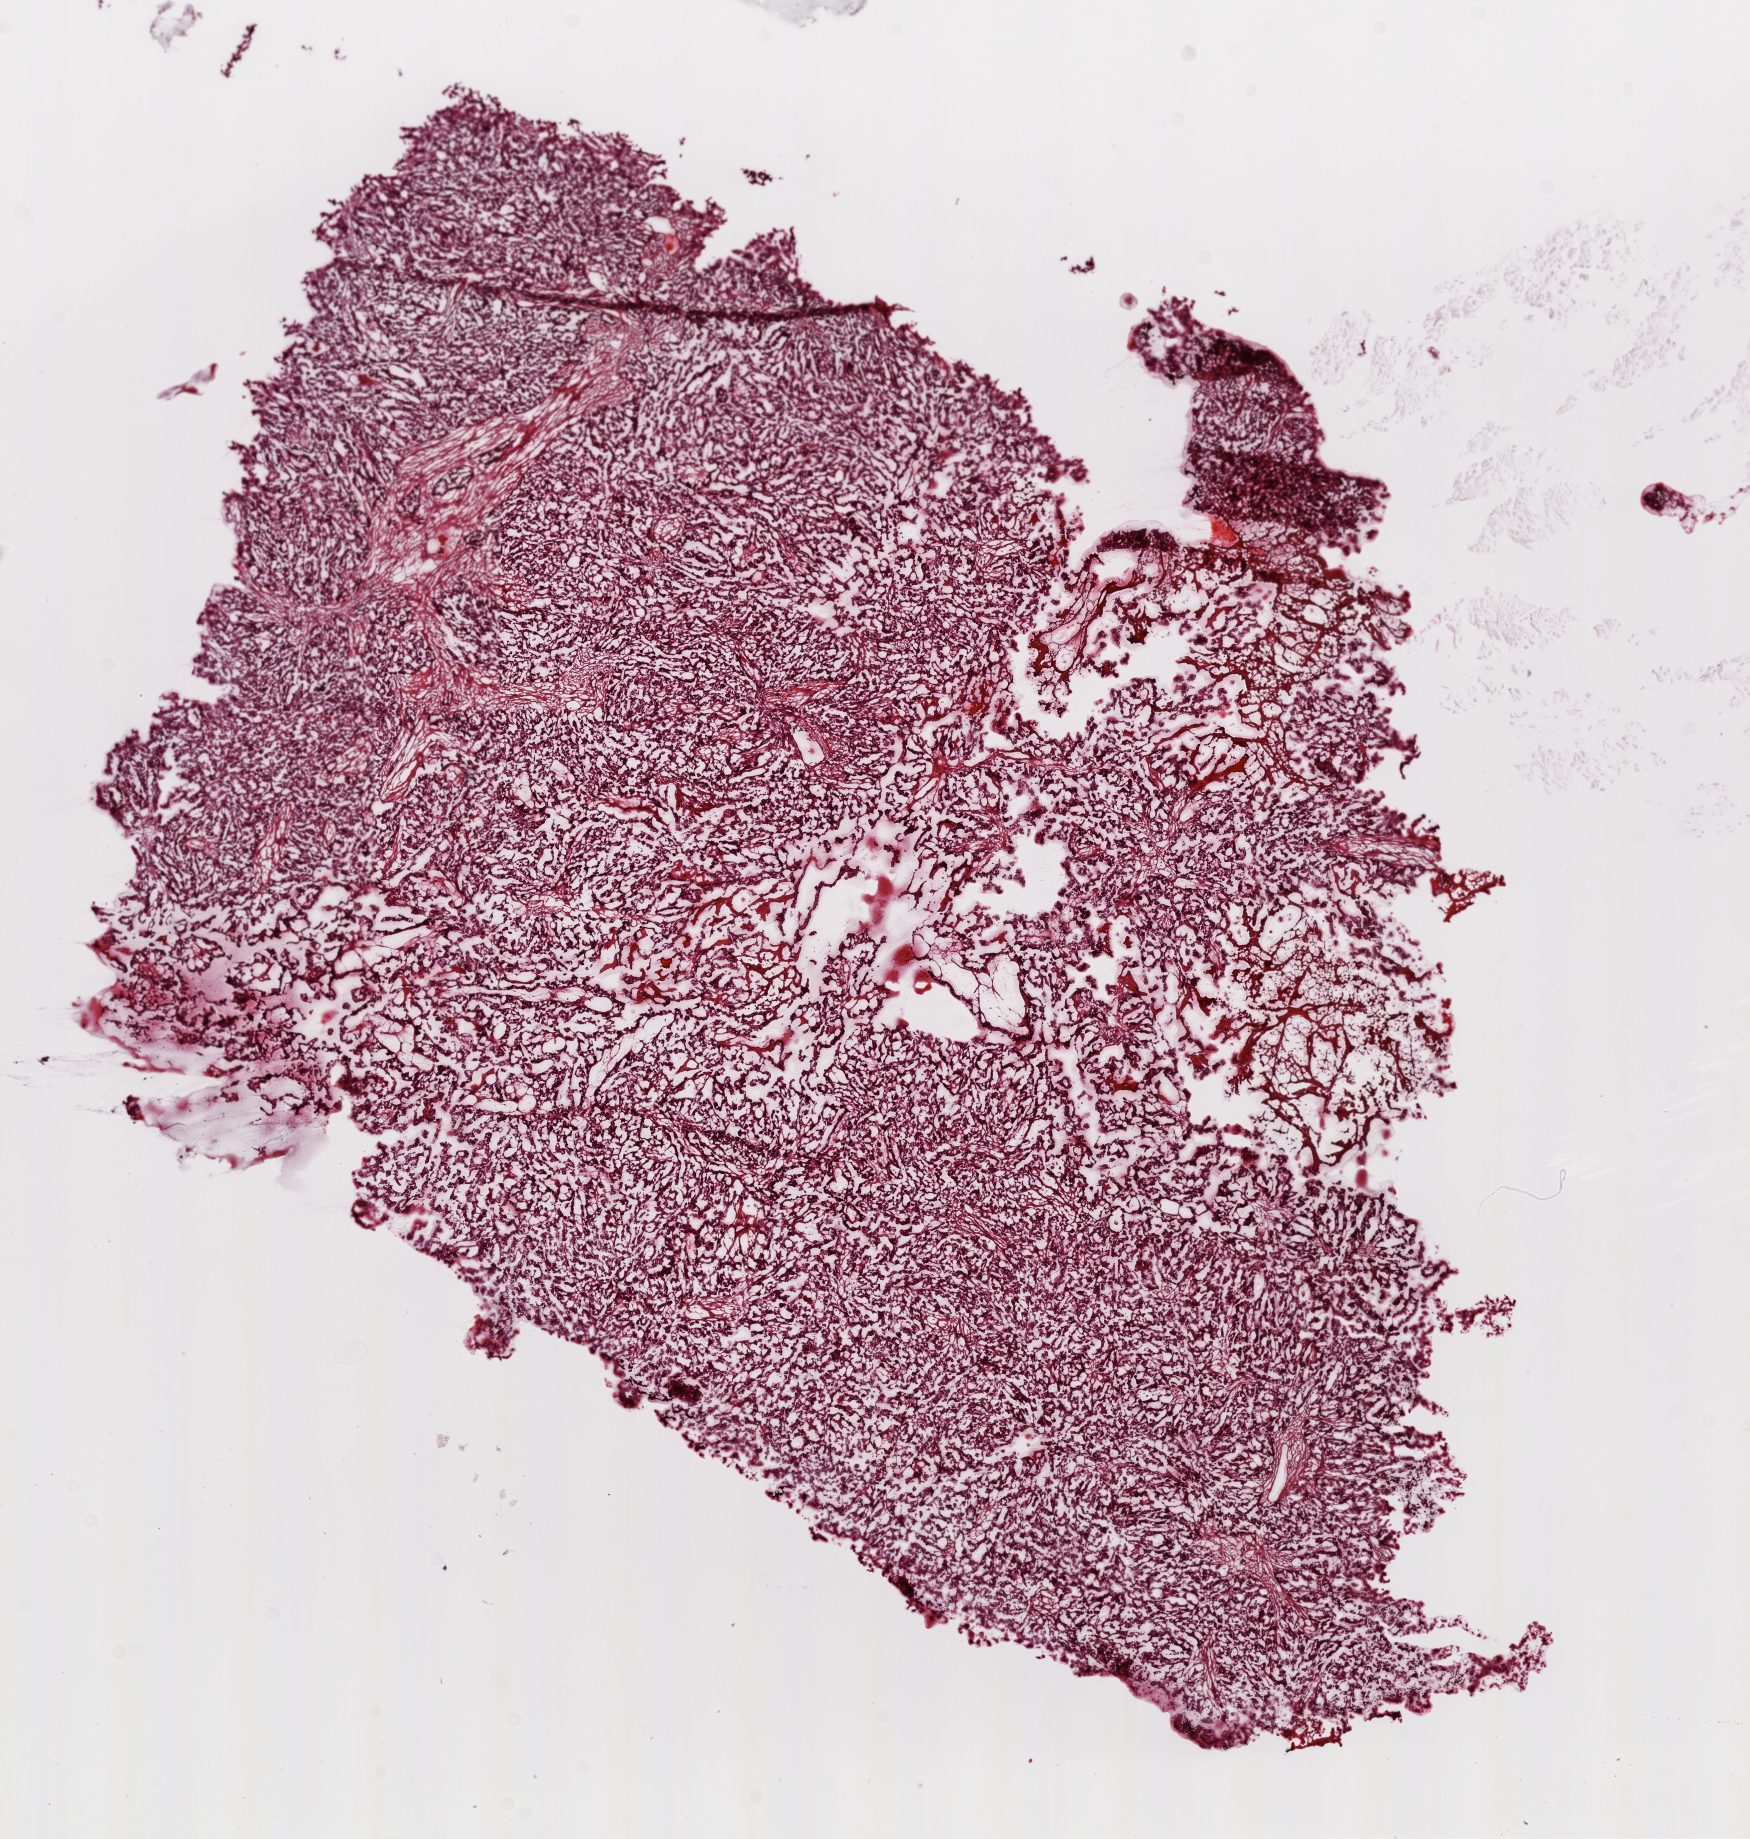
H&E whole-slide image, shown as a low-resolution overview of the whole scanned area (about 14.0 x 14.8 mm, acquisition: 20x scan). Frozen section. Primary tumour sample from the ovary. Female patient. Histologic grade: G3 (poorly differentiated). Pathologist review of this section (percent, as recorded): tumour cells 90%, tumour nuclei 80%, normal cells 0%, stromal cells 10%, necrosis 0%. Infiltration values recorded for this section: lymphocyte infiltration 0%, monocyte infiltration 0%, neutrophil infiltration 0%.
Histologic diagnosis: Serous cystadenocarcinoma, NOS. FIGO stage: IIIC.